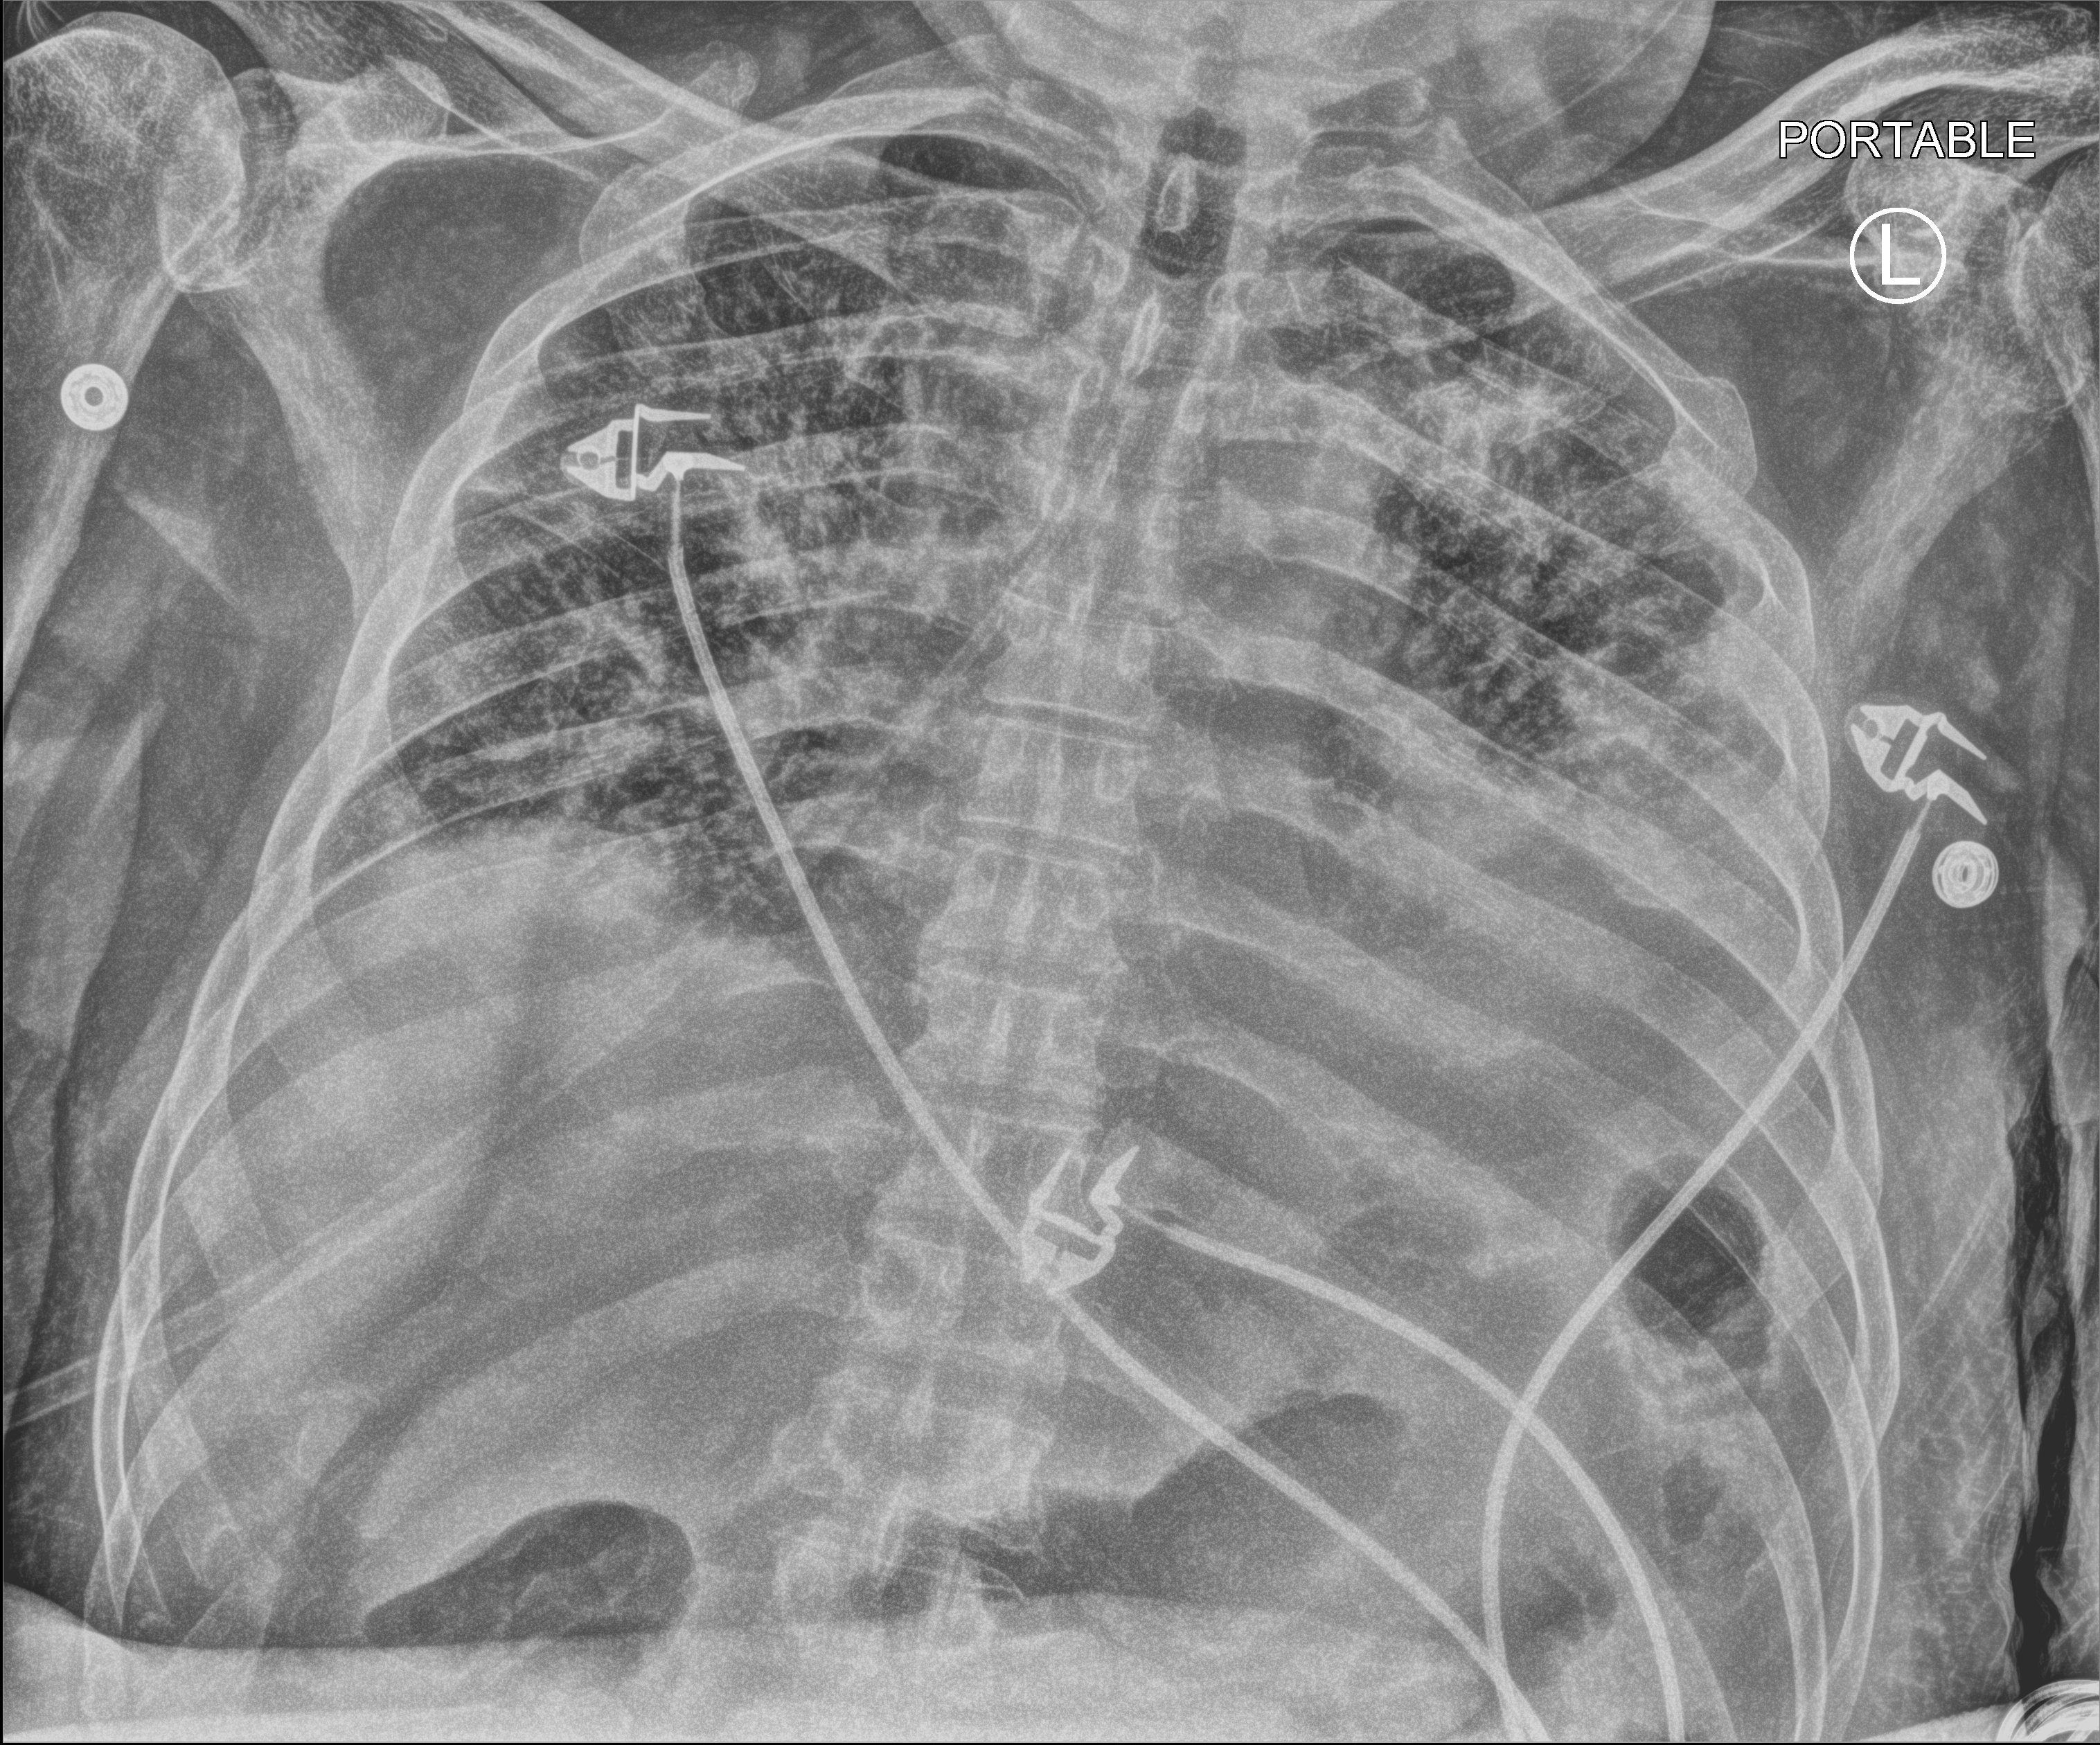
Bedside chest radiograph (computed radiography), anteroposterior (AP) projection. Patient hospitalised with COVID-19; male, aged 60–74 years.
Hospital-stay facts (about this admission, not read from this image; timing relative to this image not recorded):
- admitted to intensive care during this hospital stay: no
- length of hospital stay: 27 days
- hypertension (admission record): yes